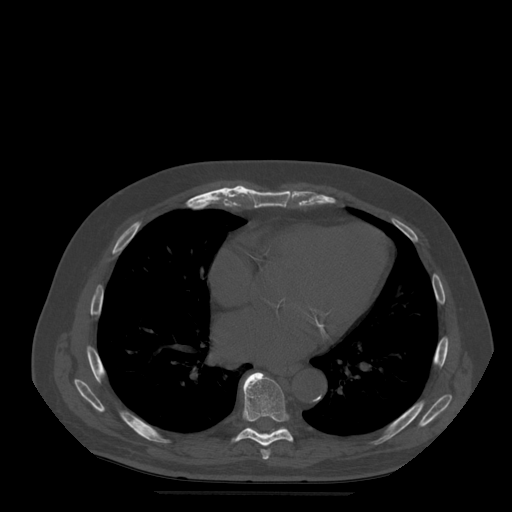
CT including the spine, one axial slice; position 310 of 522 along the scan axis; bone window (W 1800 / L 400 HU); 1.25 mm slice thickness; 512 × 512 image matrix, field of view 420 × 420 mm. Patient age 72 years. From the clinical record (not read from this slice): primary cancer: prostate.
Annotated regions visible in this slice (semi-automatically segmented with operator editing):
- T7 vertebra: bounding box (x1, y1, x2, y2) in pixels: (261, 450, 271, 460)
- T8 vertebra: (233, 372, 294, 447)
- T9 vertebra: (247, 428, 287, 432)